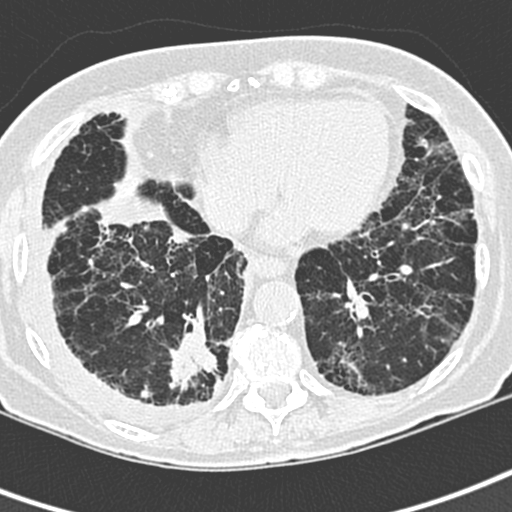
Low-dose screening chest CT, one axial slice. Slice 87 of 220 in the series (ordered by position). 120 kVp. Lung window (W 1500 / L -600 HU). 512 × 512 image matrix, field of view 288 × 288 mm.
Annotated regions visible in this slice (outlined manually by an expert reader):
- lesion 1 (tumor, lower lobe of right lung): bounding box <170,346,217,391> (left, top, right, bottom; pixels)